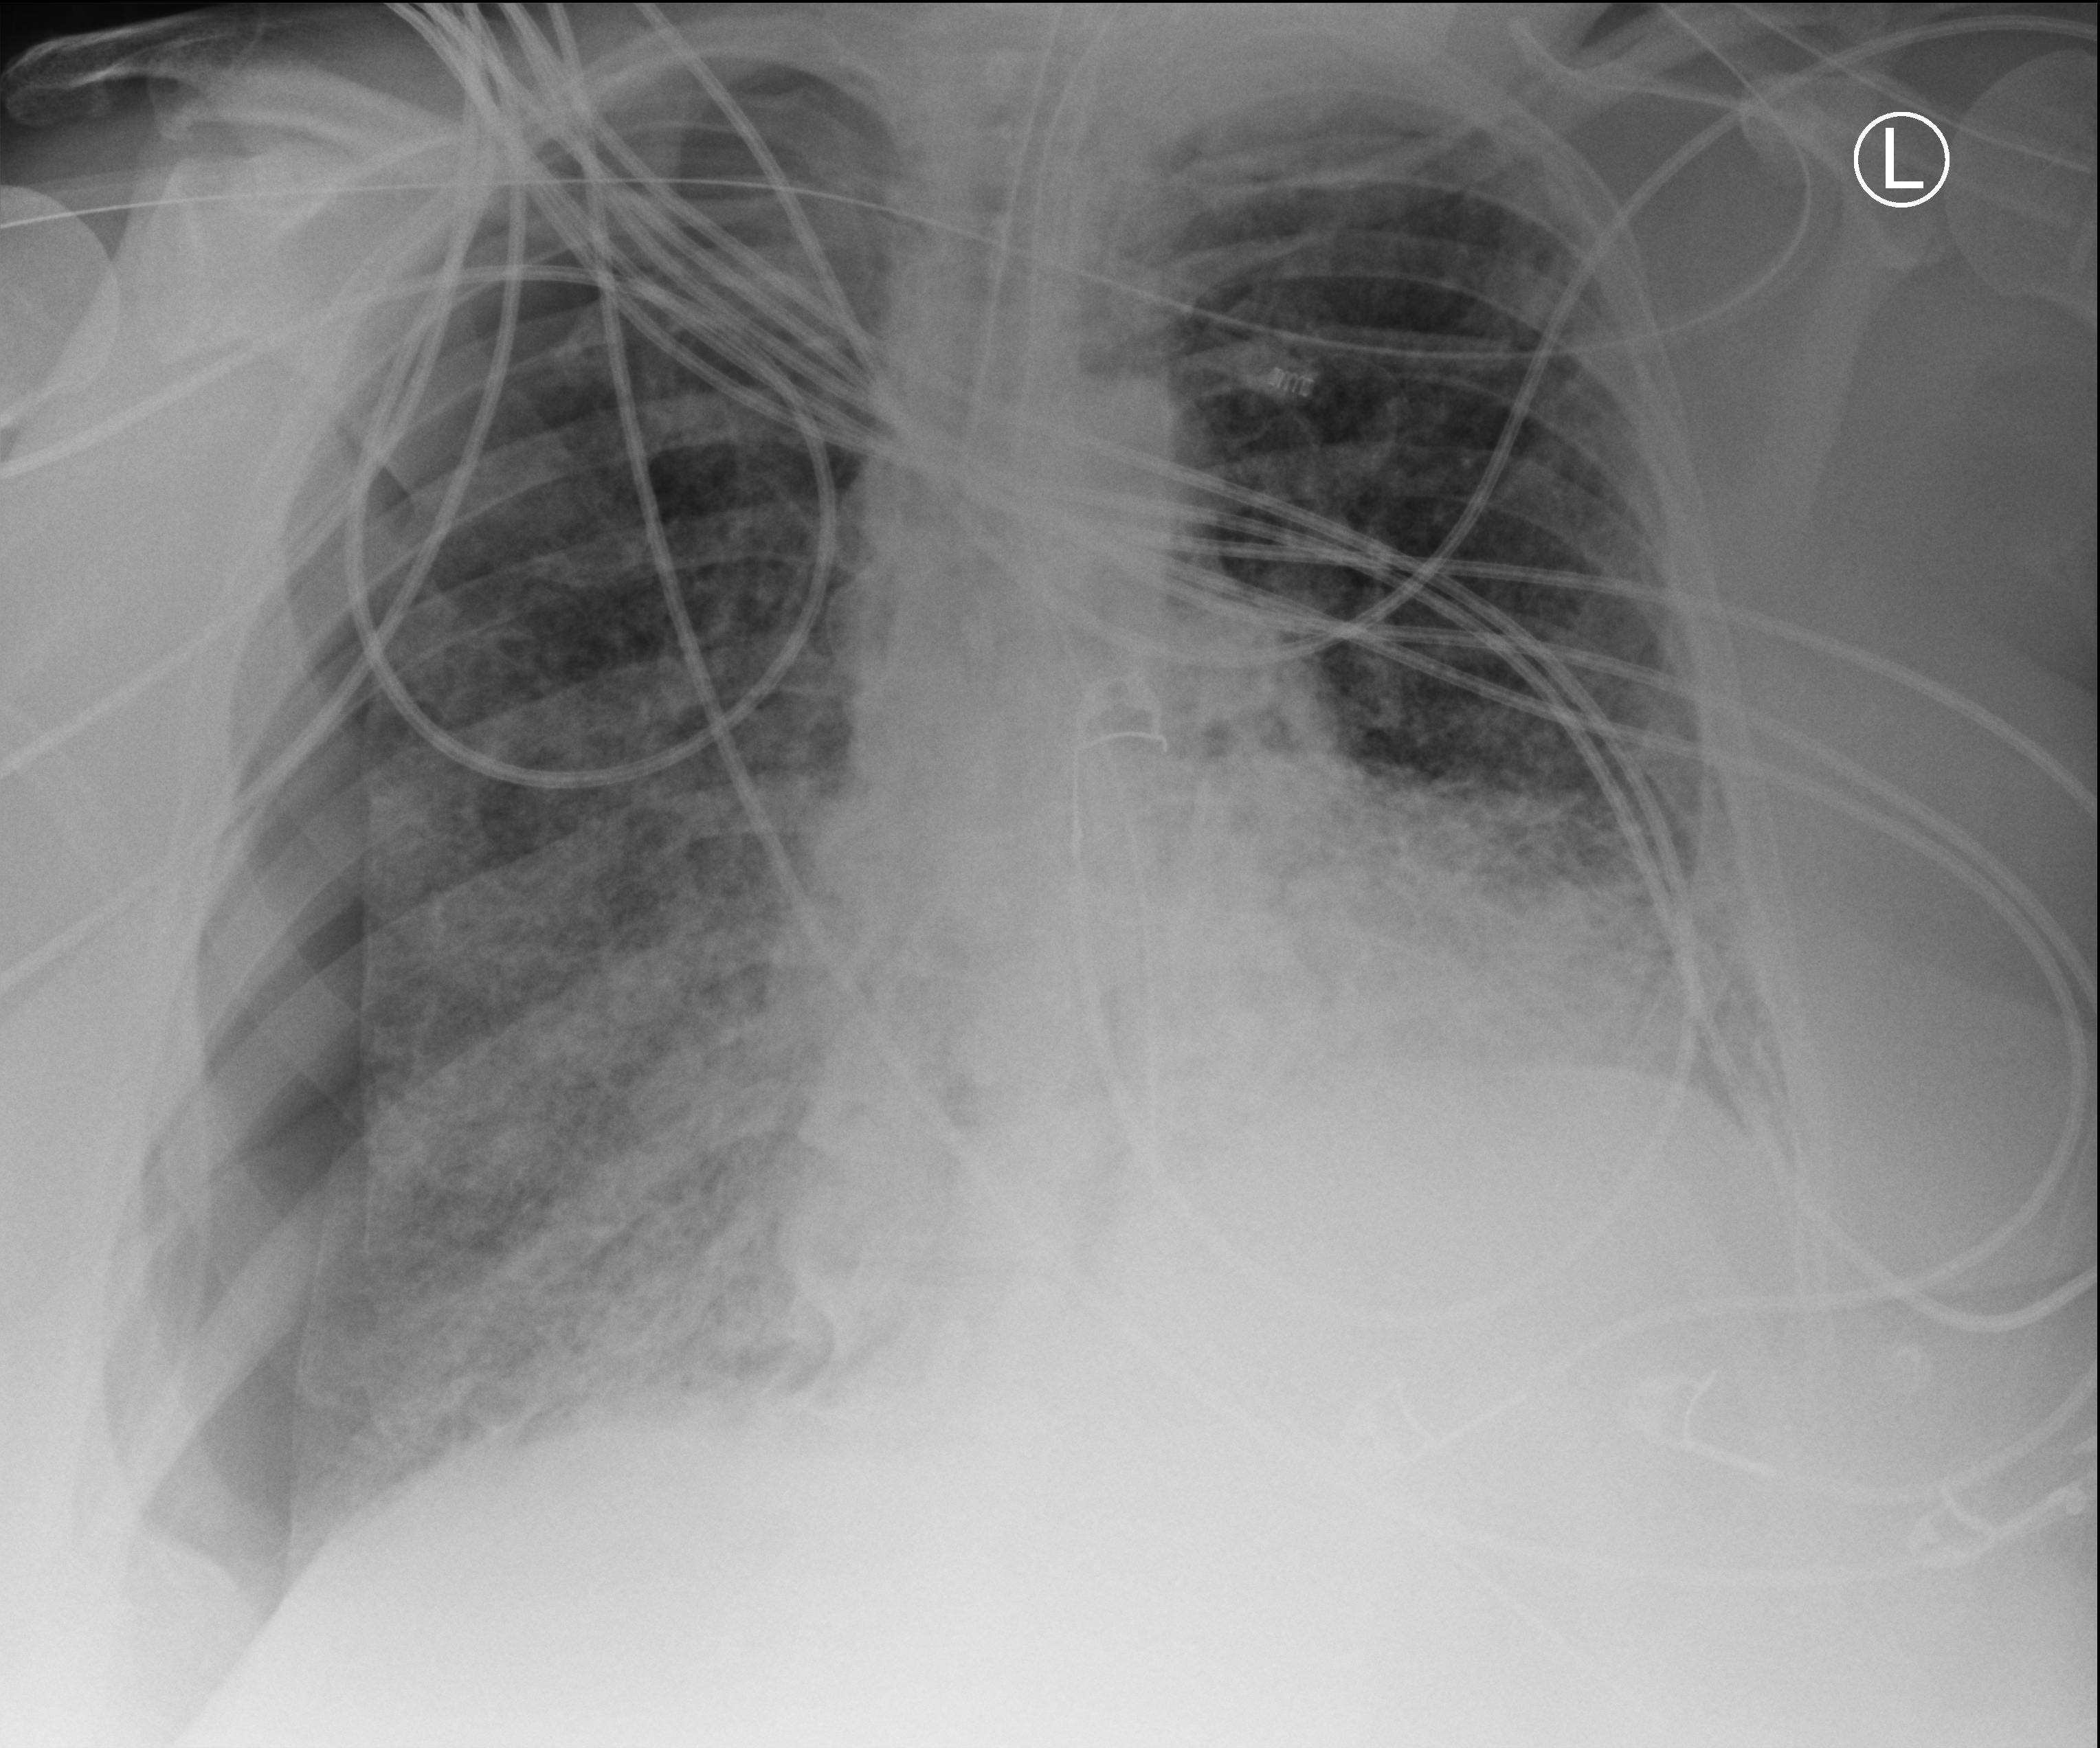
Chest X-ray (portable). Adult patient hospitalised with COVID-19, age 18–59 years.
Hospital-stay facts (about this admission, not read from this image; timing relative to this image not recorded):
- admitted to intensive care during this hospital stay: yes